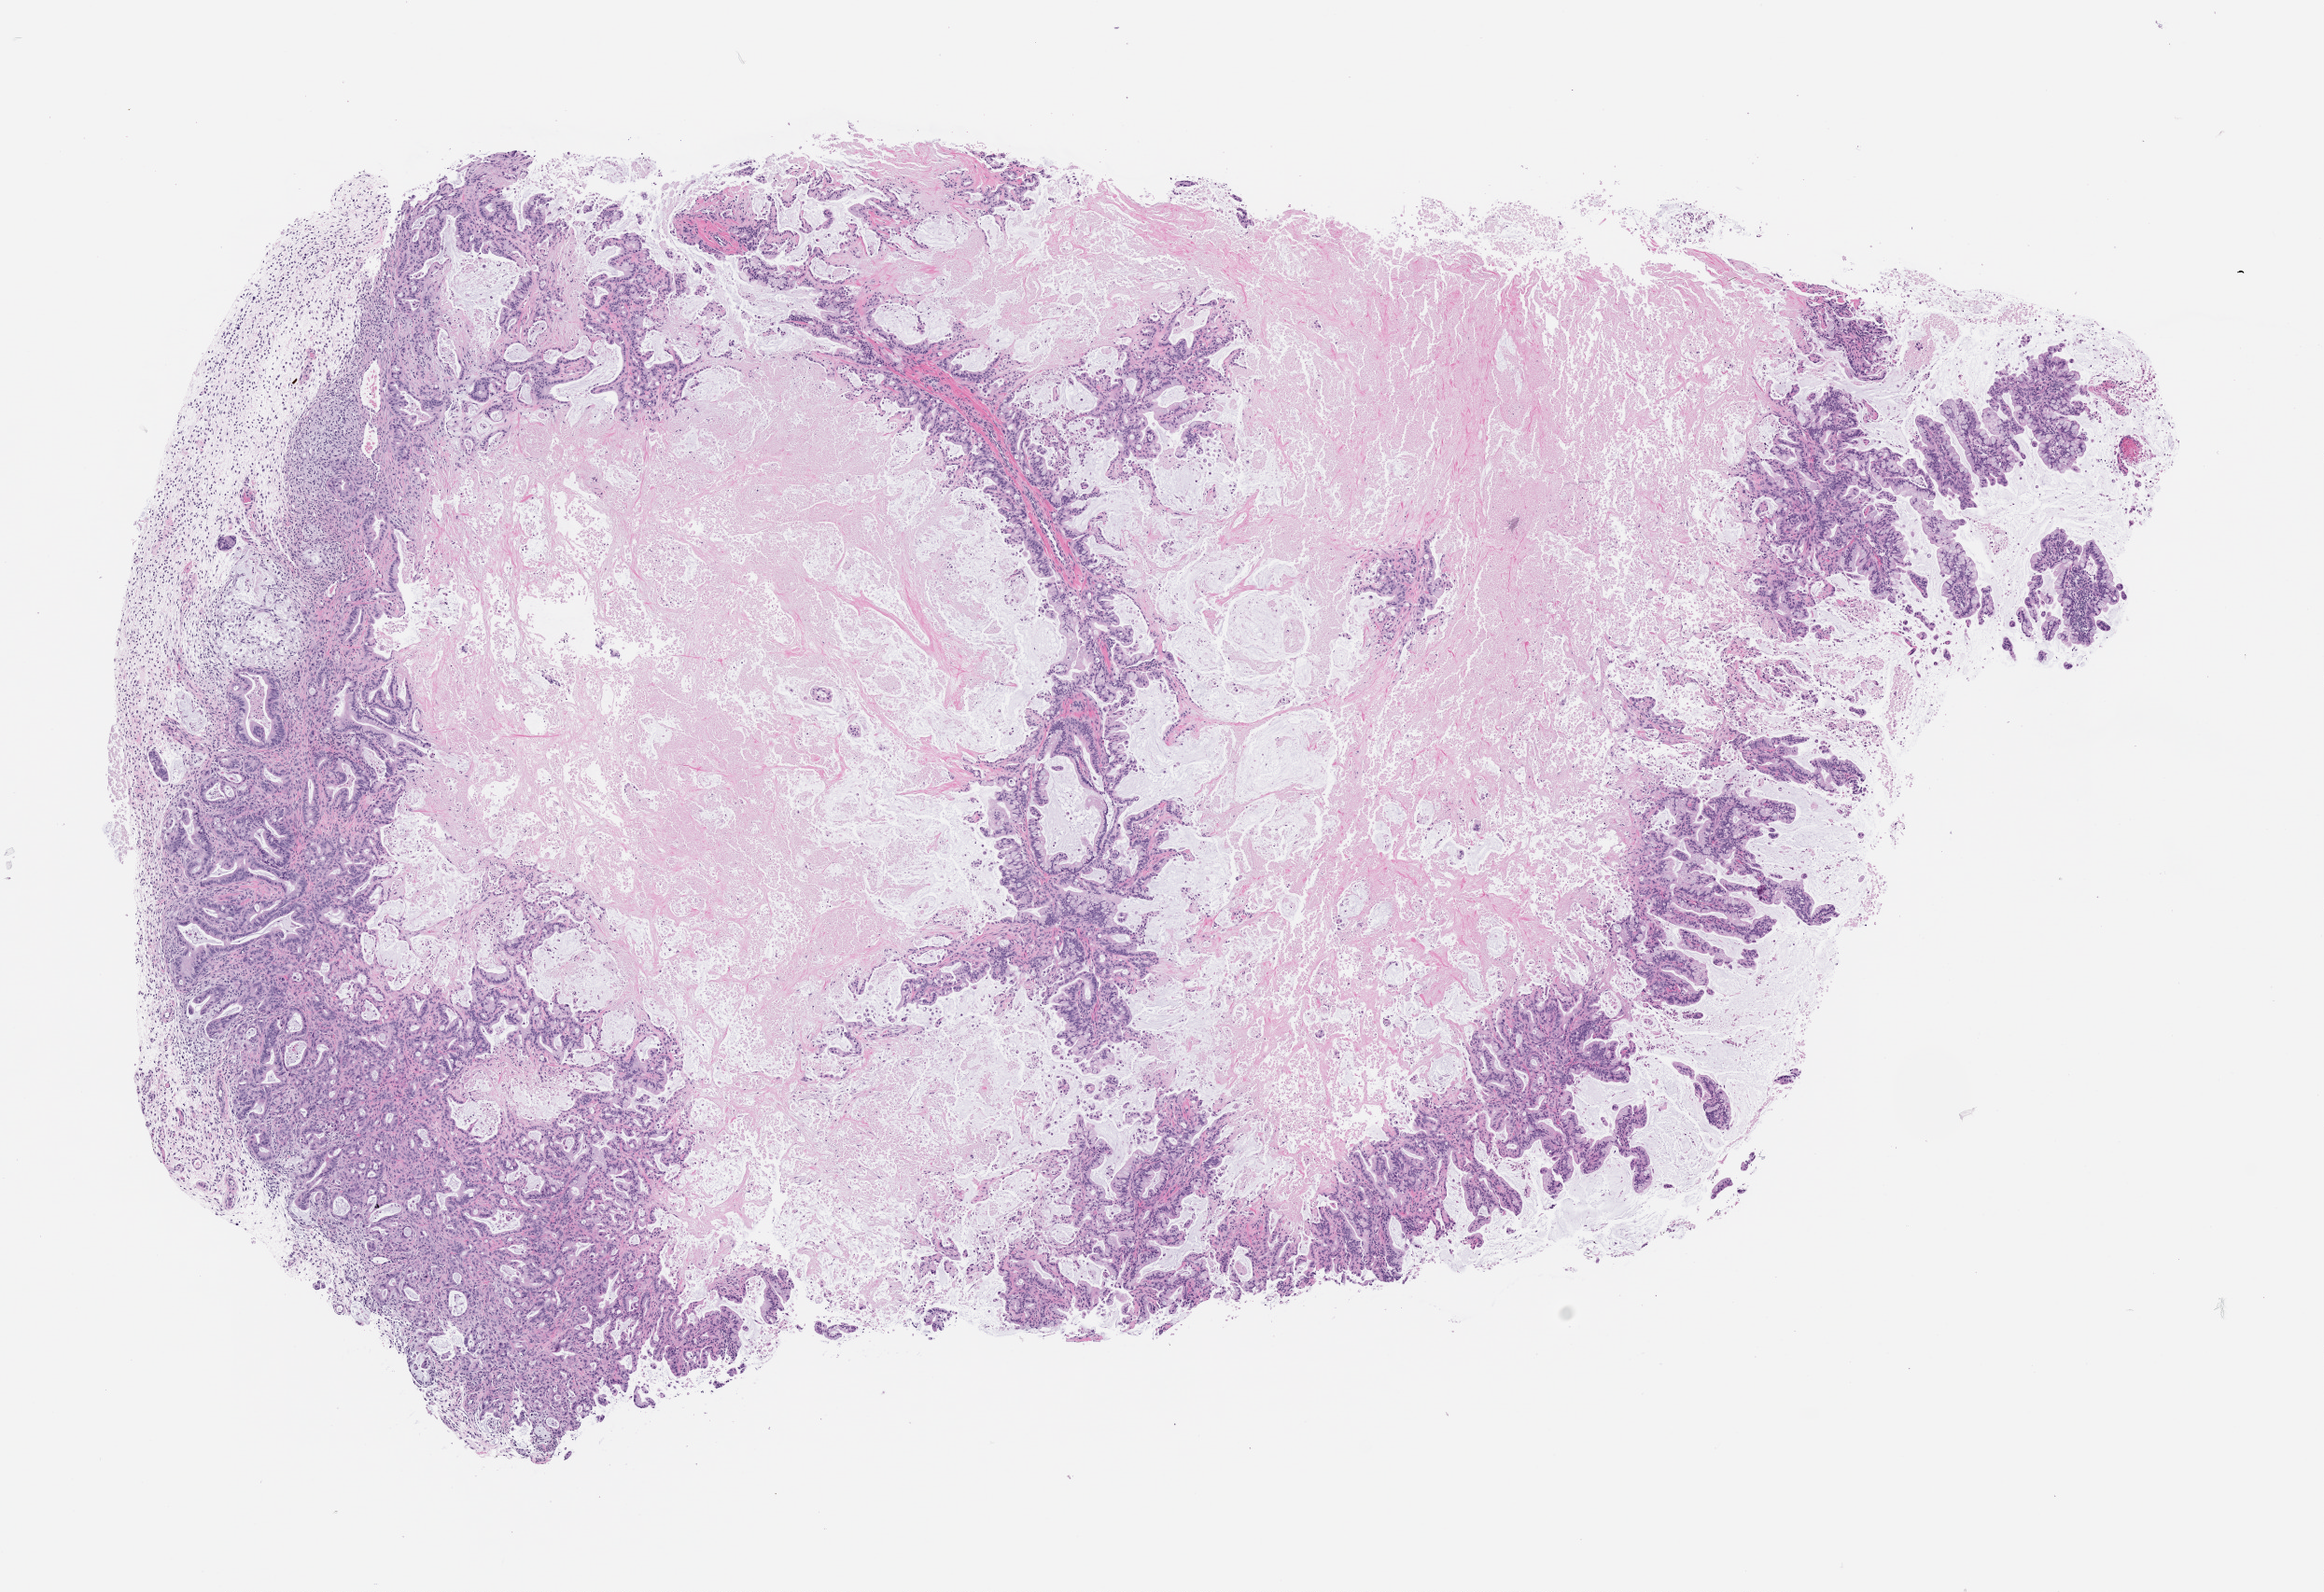
Haematoxylin and eosin whole-slide image of a patient-derived xenograft (PDX) tumor grown in a mouse, passage 3, shown as a low-resolution overview of the whole scanned area (about 10.0 x 6.9 mm); formalin-fixed paraffin-embedded section; originating tumor site category: pancreas.
Originating patient diagnosis: Pancreatic Adenocarcinoma.